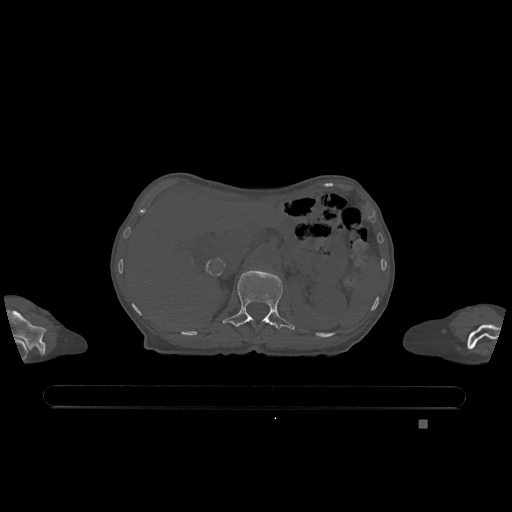
CT including the spine, one axial slice. Position 478 of 1317 along the scan axis. Bone window (W 1800 / L 400 HU). 0.5 mm slice thickness. 512 × 512 image matrix, field of view 500 × 500 mm. Patient: female, 74 years. Case-level facts recorded for this patient, not image findings: primary cancer: lung; vertebrae with lytic lesions (as recorded): T1, T4, T5, T6, L4, L5.
Annotated regions visible in this slice (semi-automatic segmentation, software-assisted and operator-edited):
- L1 vertebra: bounding box [x1, y1, x2, y2] px = [222, 269, 295, 330]